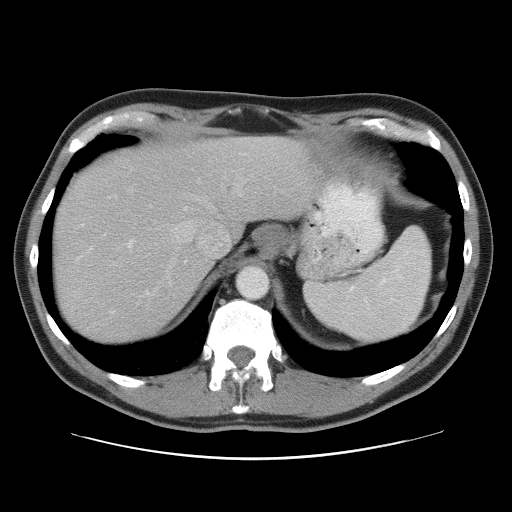
Contrast-enhanced abdominal CT, one axial slice. Position 44 of 52 along the scan axis. Reconstruction kernel STANDARD. 120 kVp. Intravenous contrast given. Soft-tissue window (W 400 / L 40 HU). 512 × 512 image matrix. Male patient, age 70 years. From the clinical record (not read from this slice): diagnosis: colorectal cancer liver metastases, imaged before liver resection; multiple liver metastases: yes; largest metastasis: 4 cm; chemotherapy before resection: yes.
Outlined on this slice (manually delineated by an expert):
- hepatic veins: box from (x=145, y=184) to (x=242, y=296) px
- liver: (x=52, y=137)–(x=314, y=347)
- planned liver remnant (the part of the liver to remain after resection): (x=122, y=137)–(x=314, y=223)
- portal vein (with intrahepatic branches): (x=128, y=240)–(x=133, y=246)